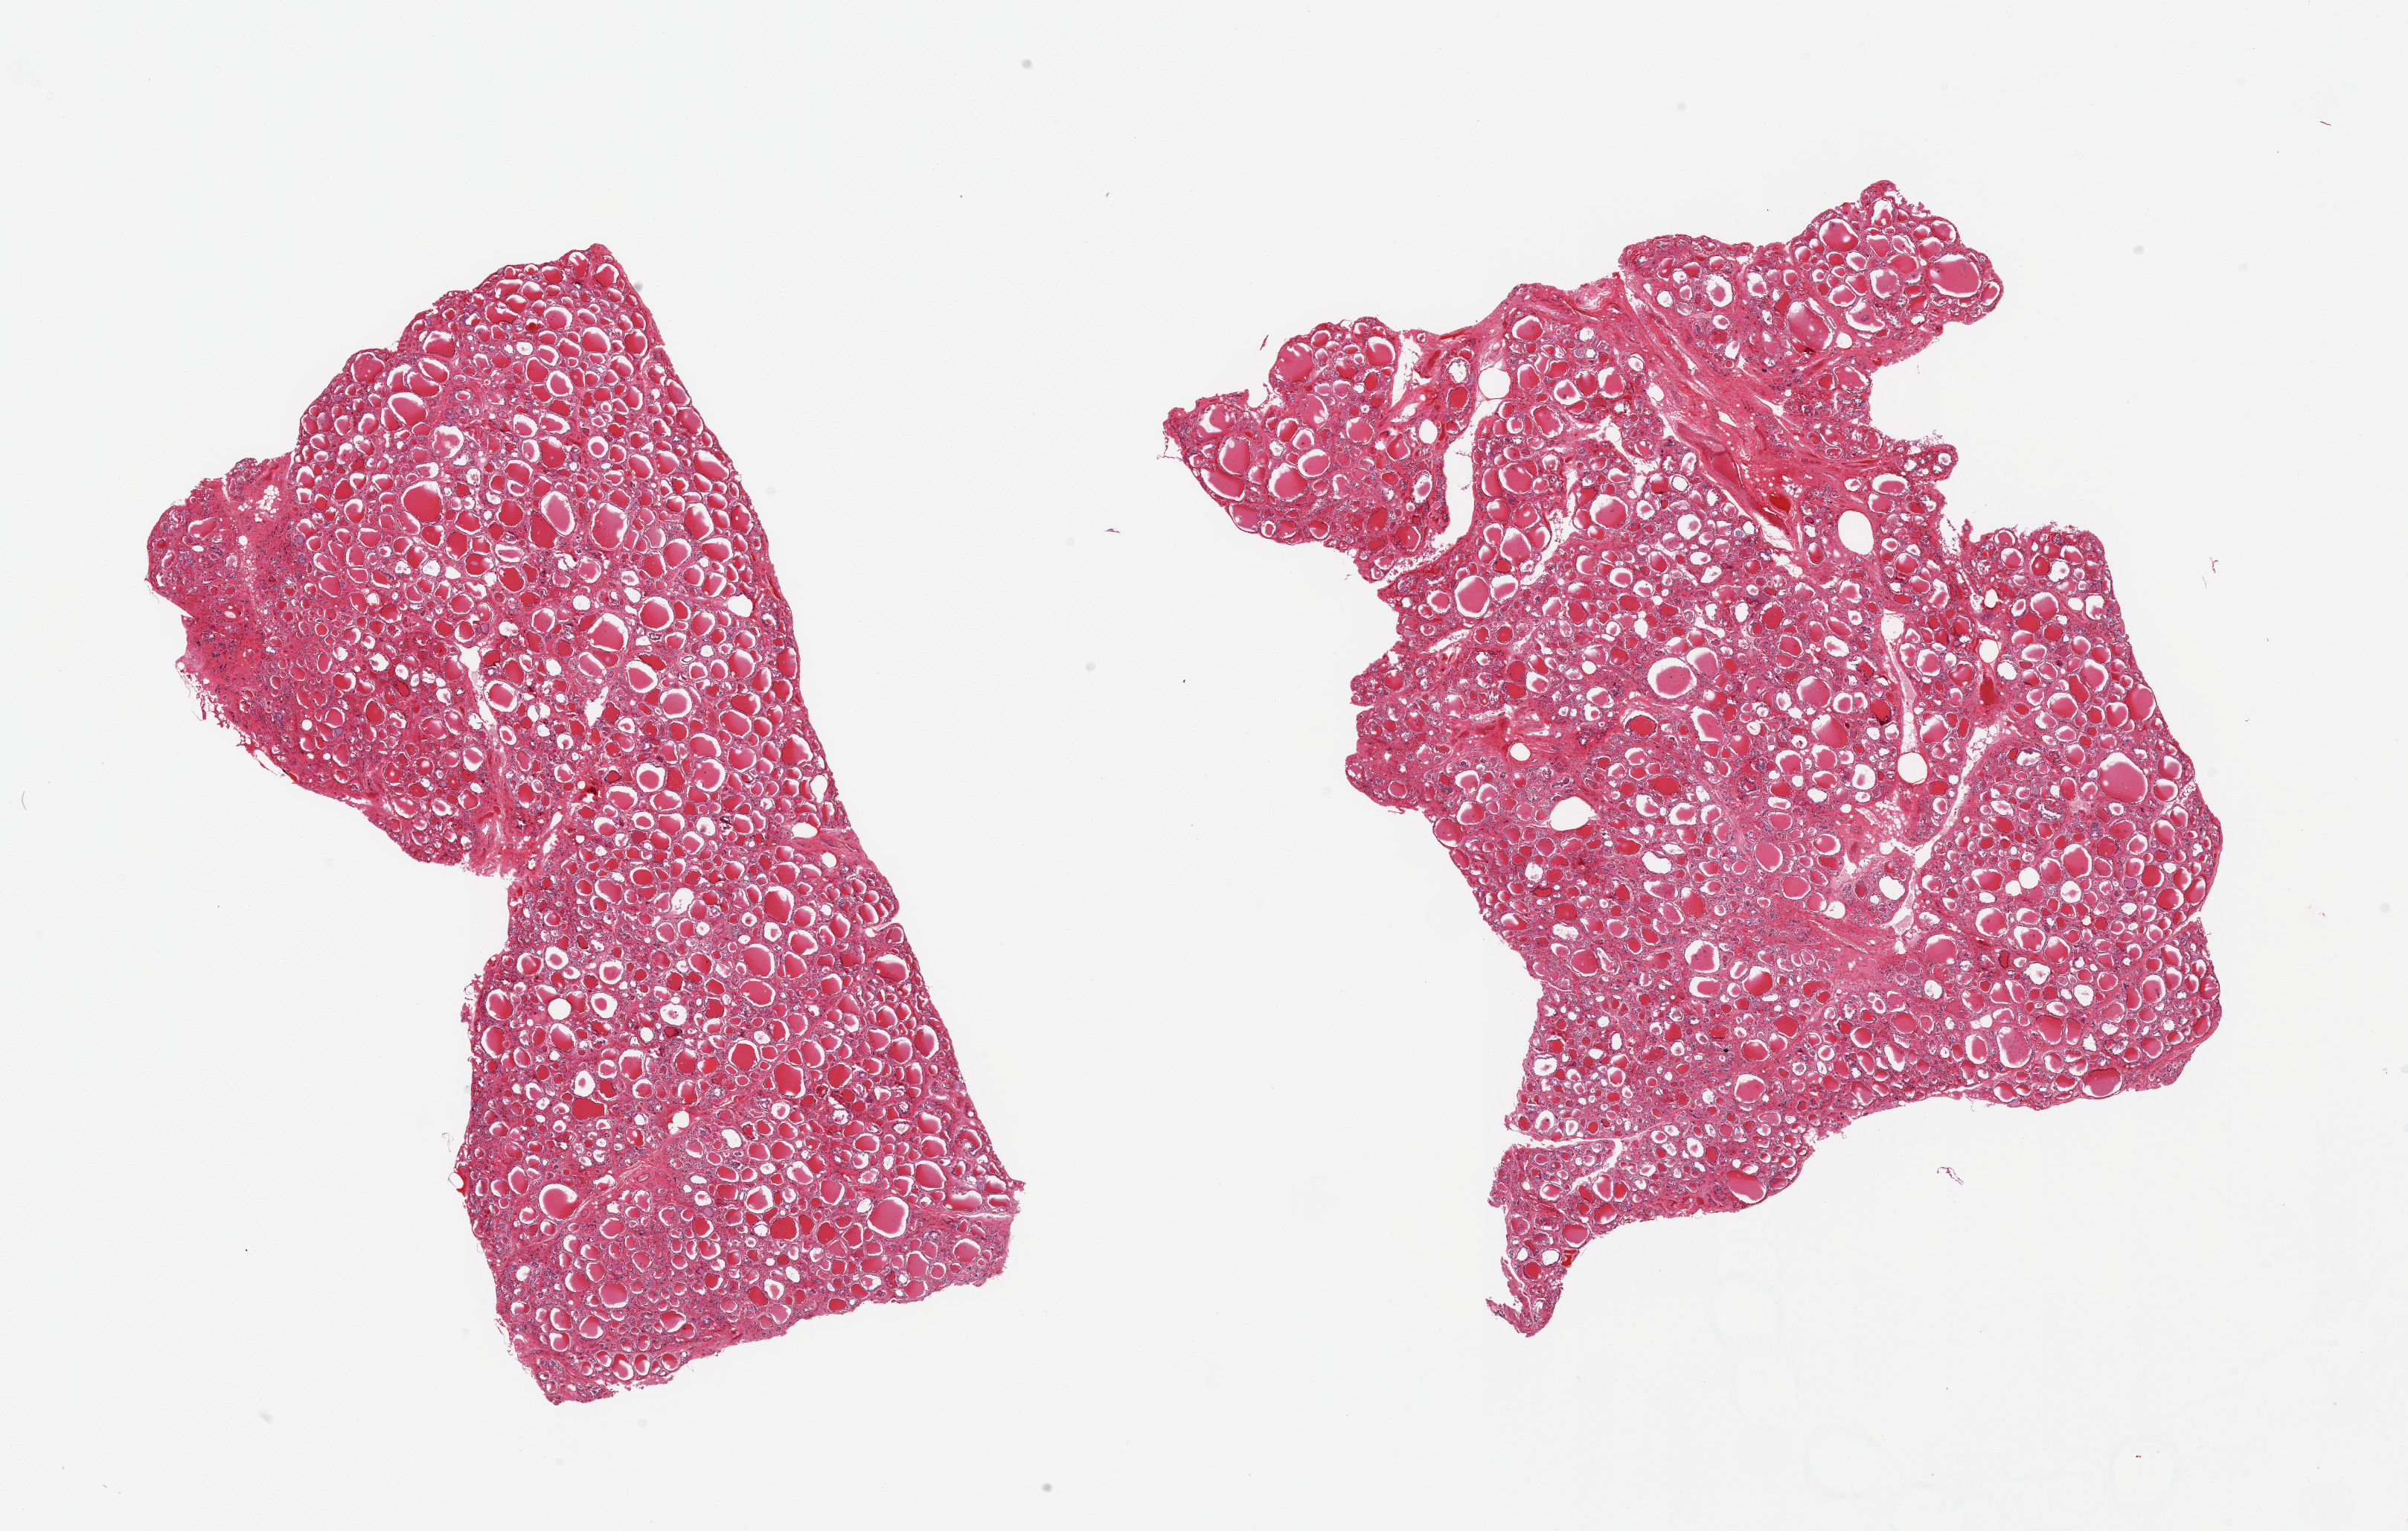
Whole-slide image, haematoxylin and eosin stain — shown as a low-resolution overview of the whole scanned area (about 25.6 x 16.3 mm); PAXgene-fixed paraffin-embedded (PFPE) section; section of thyroid (target tissue); tissue donor sample. Male donor.
Pathologist's review note for this sample: 2 pieces.